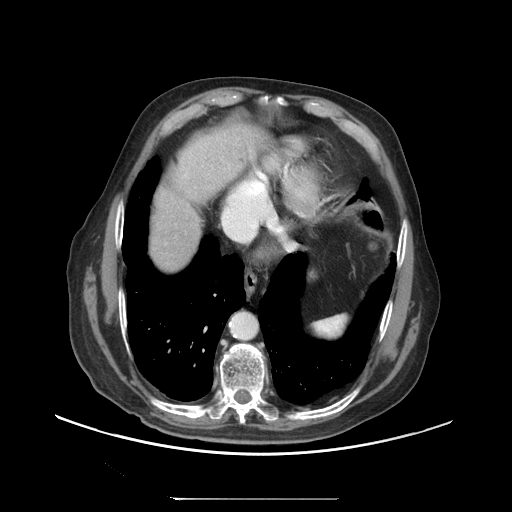
Contrast-enhanced abdominal CT (liver protocol), one axial slice; position 86 of 97 along the scan axis; soft-tissue window (W 400 / L 40 HU); 2.5 mm slice thickness; 512 × 512 image matrix, field of view 450 × 450 mm. From the clinical record (not read from this slice): diagnosis: hepatocellular carcinoma (patient treated with transarterial chemoembolisation; whether this scan precedes or follows treatment is not stated here); TNM stage (as recorded): Stage-IIIC; Child-Pugh class: A; tumour differentiation: well differentiated; tumour nodularity: uninodular.
Structures marked on this image (semi-automatically segmented with operator editing):
- abdominal aorta: bounding box <231,312,256,339> (left, top, right, bottom; pixels)
- liver parenchyma outside the tumour (the mass and vessels are separate outlines, so this box may not span the whole liver): <150,180,214,270>